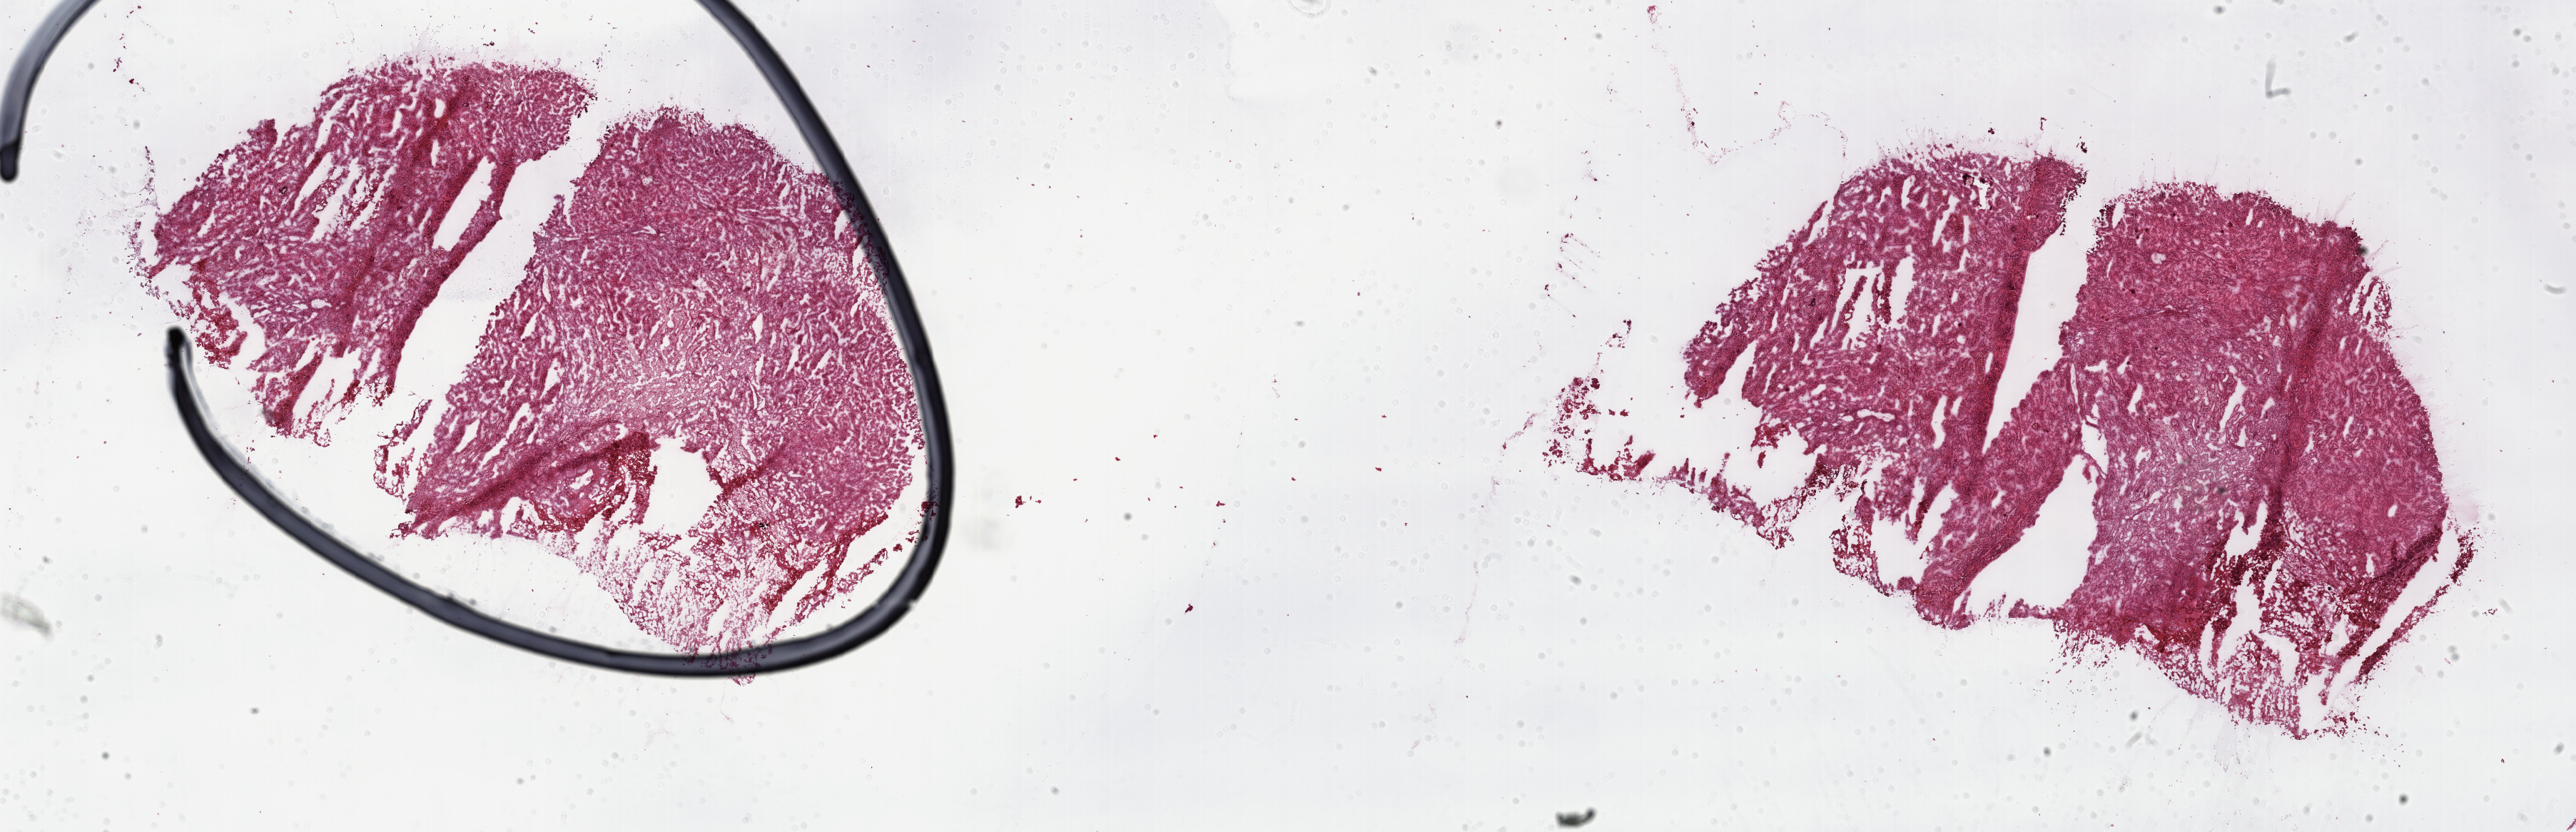
Hematoxylin and eosin (H&E) stained whole-slide image — a low-resolution overview of the entire scanned area, about 29.2 x 9.4 mm (acquisition: 40x scan); frozen section from the top of the tissue portion; sample: primary tumour, kidney. Patient: male, age at initial diagnosis 62 years. Slide review estimates, as recorded: tumour cells 100%, tumour nuclei 75%, normal cells 0%, stromal cells 0%, necrosis 0%. Inflammatory infiltration, as recorded: lymphocyte infiltration 1%, monocyte infiltration 8%, neutrophil infiltration 0%.
* histologic diagnosis: Papillary adenocarcinoma, NOS